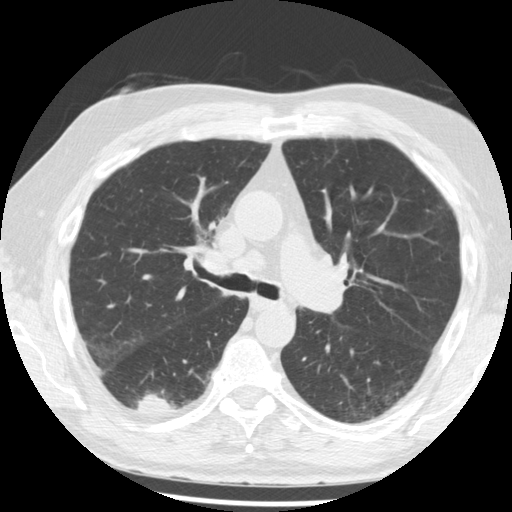
Axial slice from a low-dose chest CT screening exam. Third annual screen. Lung window (W 1500 / L -600 HU). 2.5 mm slice thickness. Standard (soft-tissue) reconstruction kernel (STANDARD). 512 × 512 image matrix. Male participant, aged 68 years at enrolment. Current smoker at enrolment.
Lesion marked by an expert reader, bounding box (x1, y1, x2, y2) in pixels: (123, 378, 187, 426). The screening reader recorded 3 non-calcified nodules or masses ≥4 mm on this exam; which of them this box marks is not recorded. Official screen result: positive, other. Participant outcome: lung cancer diagnosed 48 days after this screen — squamous cell carcinoma, NOS, right lower lobe, moderately differentiated (G2), stage IB (AJCC 6th edition), 20 mm at pathology.